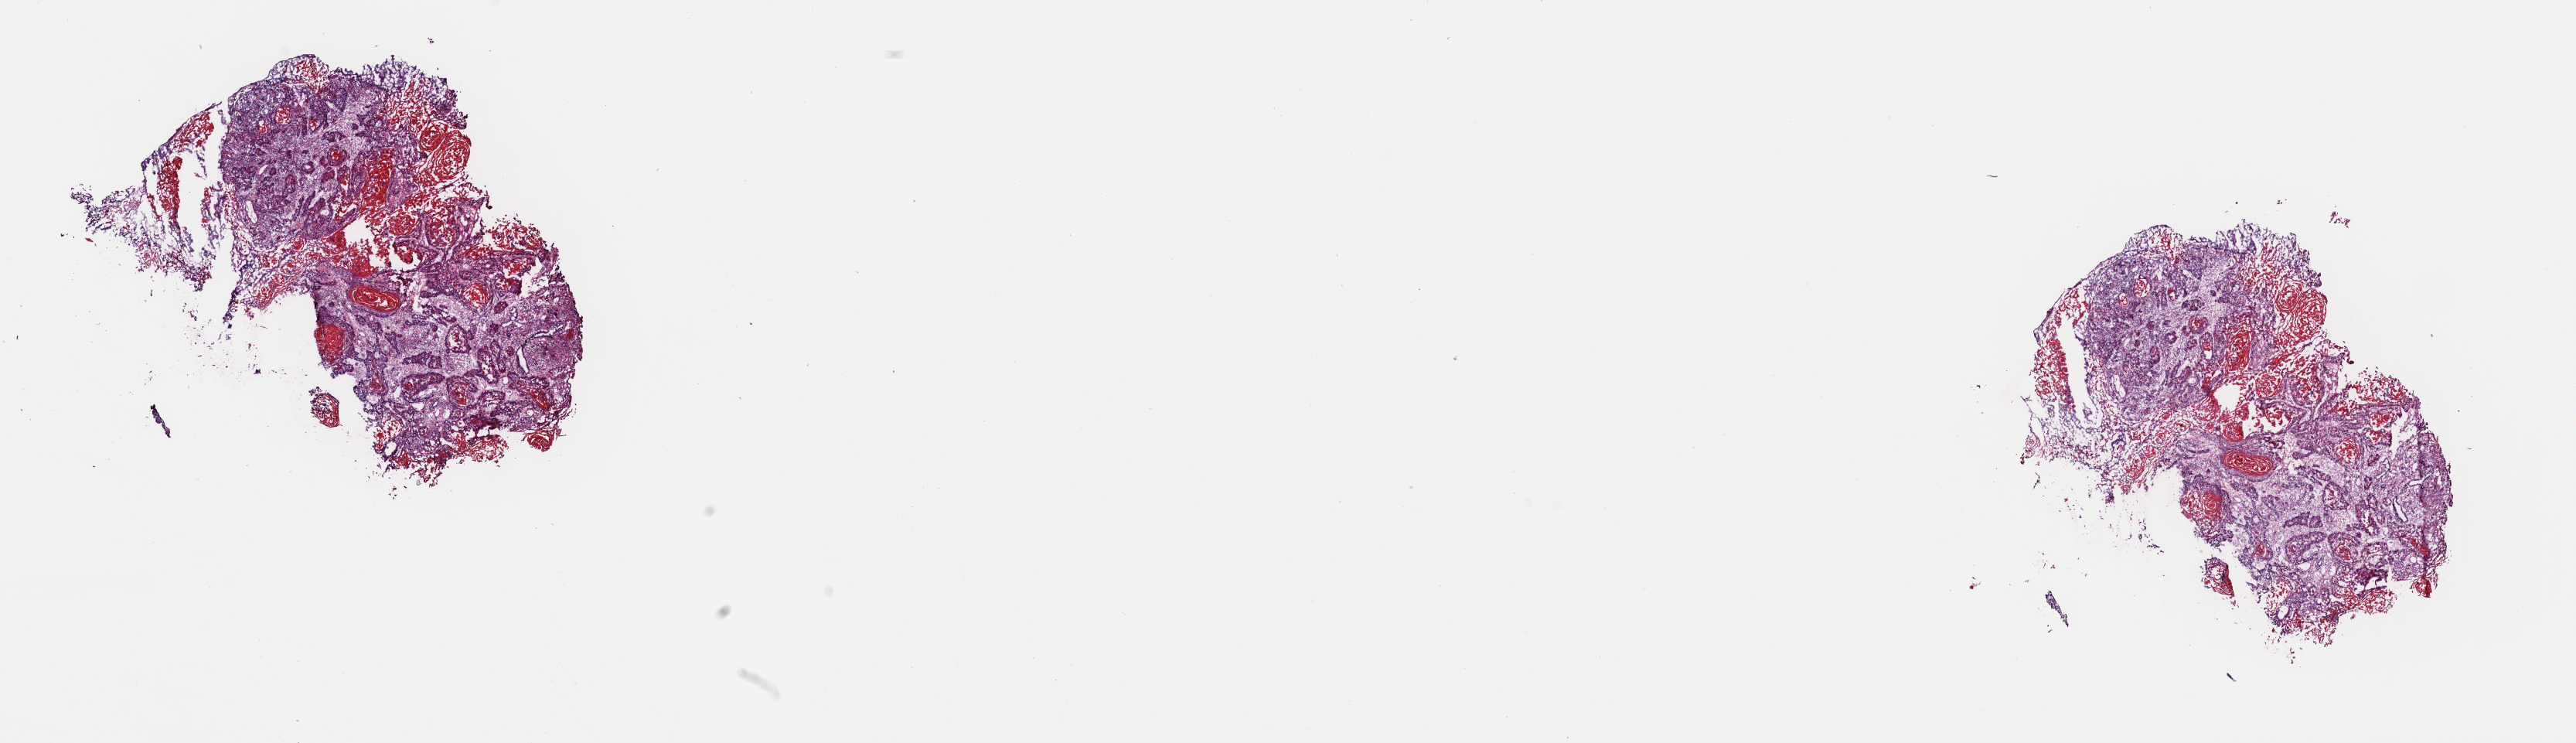
Hematoxylin and eosin (H&E) stained whole-slide image, whole scanned area (about 26.3 x 7.6 mm, slide scanned at 40x) shown as a low-resolution overview, frozen section from the top of the tissue portion, primary tumour sample from the head and neck. Female patient; age at initial diagnosis 79 years. Histologic grade: G2 (moderately differentiated). Composition of this section per pathologist review: tumour cells 100%, tumour nuclei 65%, normal cells 0%, stromal cells 0%, necrosis 0%. Inflammatory infiltration, as recorded: lymphocyte infiltration 10%, monocyte infiltration 0%, neutrophil infiltration 0%.
Histologic diagnosis: Squamous cell carcinoma, NOS. AJCC pathologic stage: IVA (6th edition).